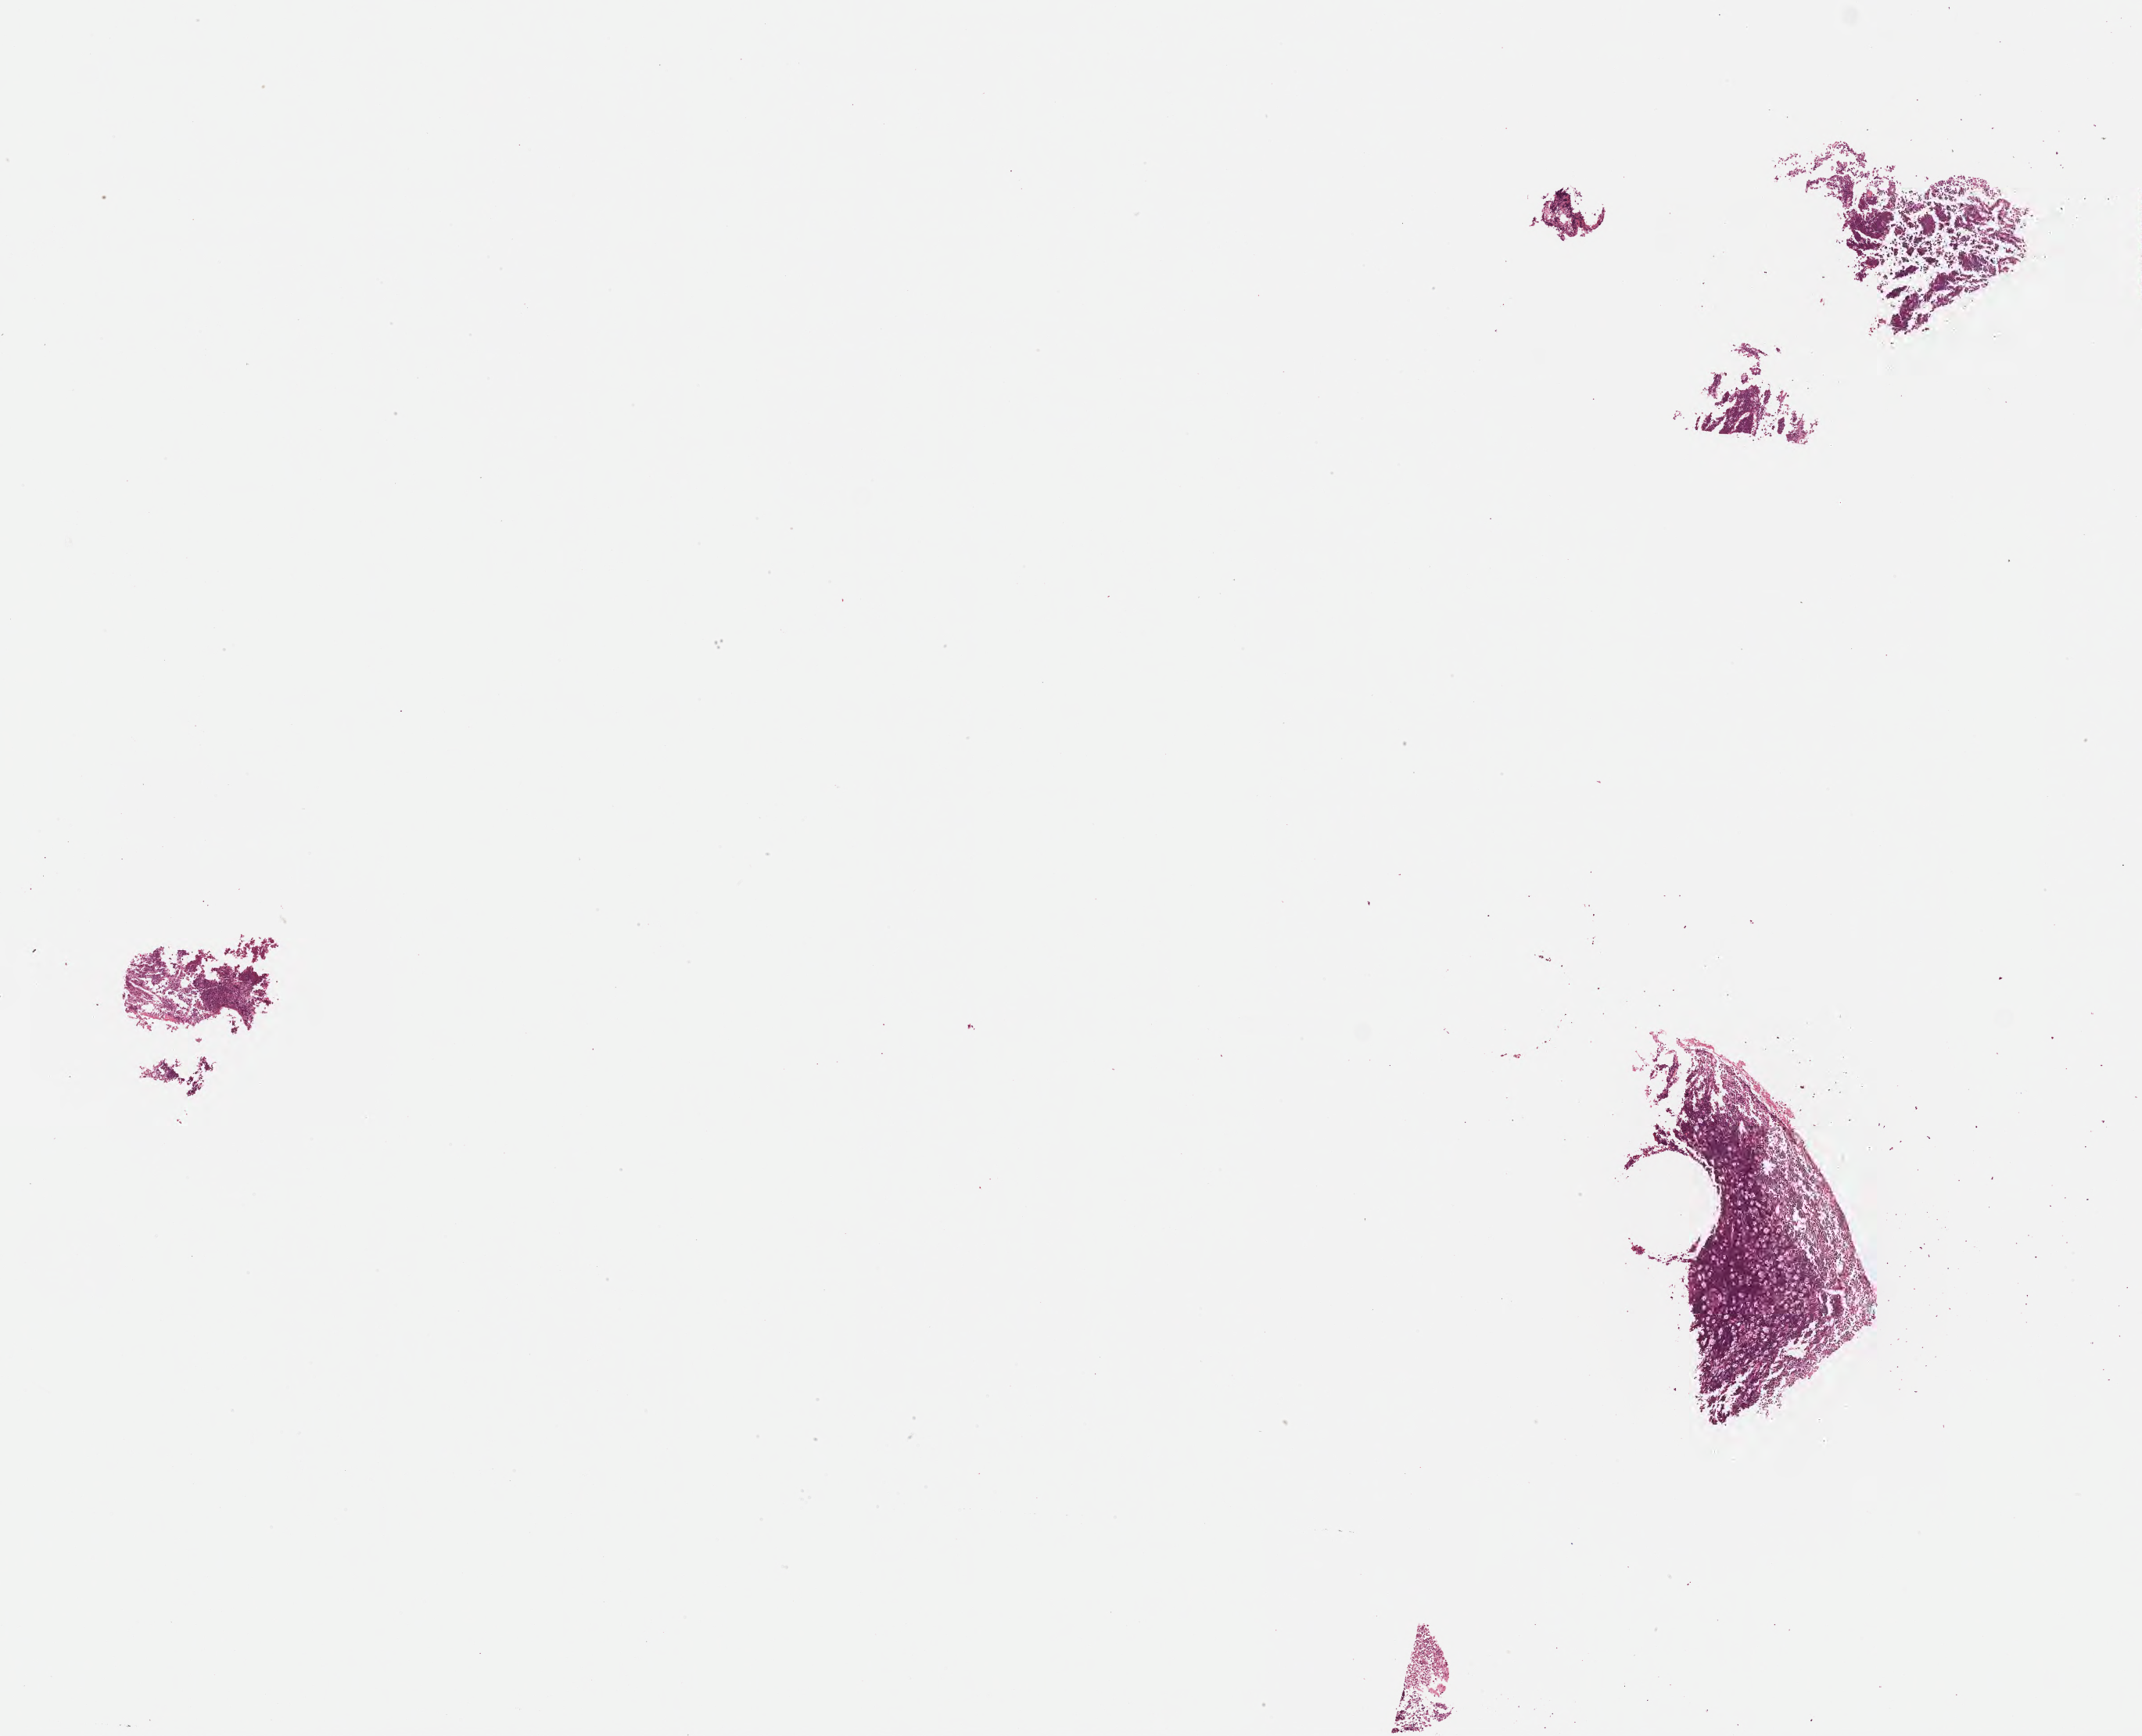
H&E whole-slide image, whole scanned area (about 11.1 x 9.0 mm) shown as a low-resolution overview; formalin-fixed, paraffin-embedded (FFPE) tissue; specimen: primary tumor. Patient male; age 11 years. Pathologist review of this section (percent, as recorded): tumor cells 75%, tumor nuclei 90%, stromal cells 15%, necrosis 0%, normal cells 10%. Inflammatory infiltration, as recorded: lymphocyte infiltration 70%, monocyte infiltration 15%, neutrophil infiltration 5%.
Ann Arbor stage (patient): Stage IV. Diagnosis: Burkitt lymphoma, NOS. Section: bottom of the tissue portion.